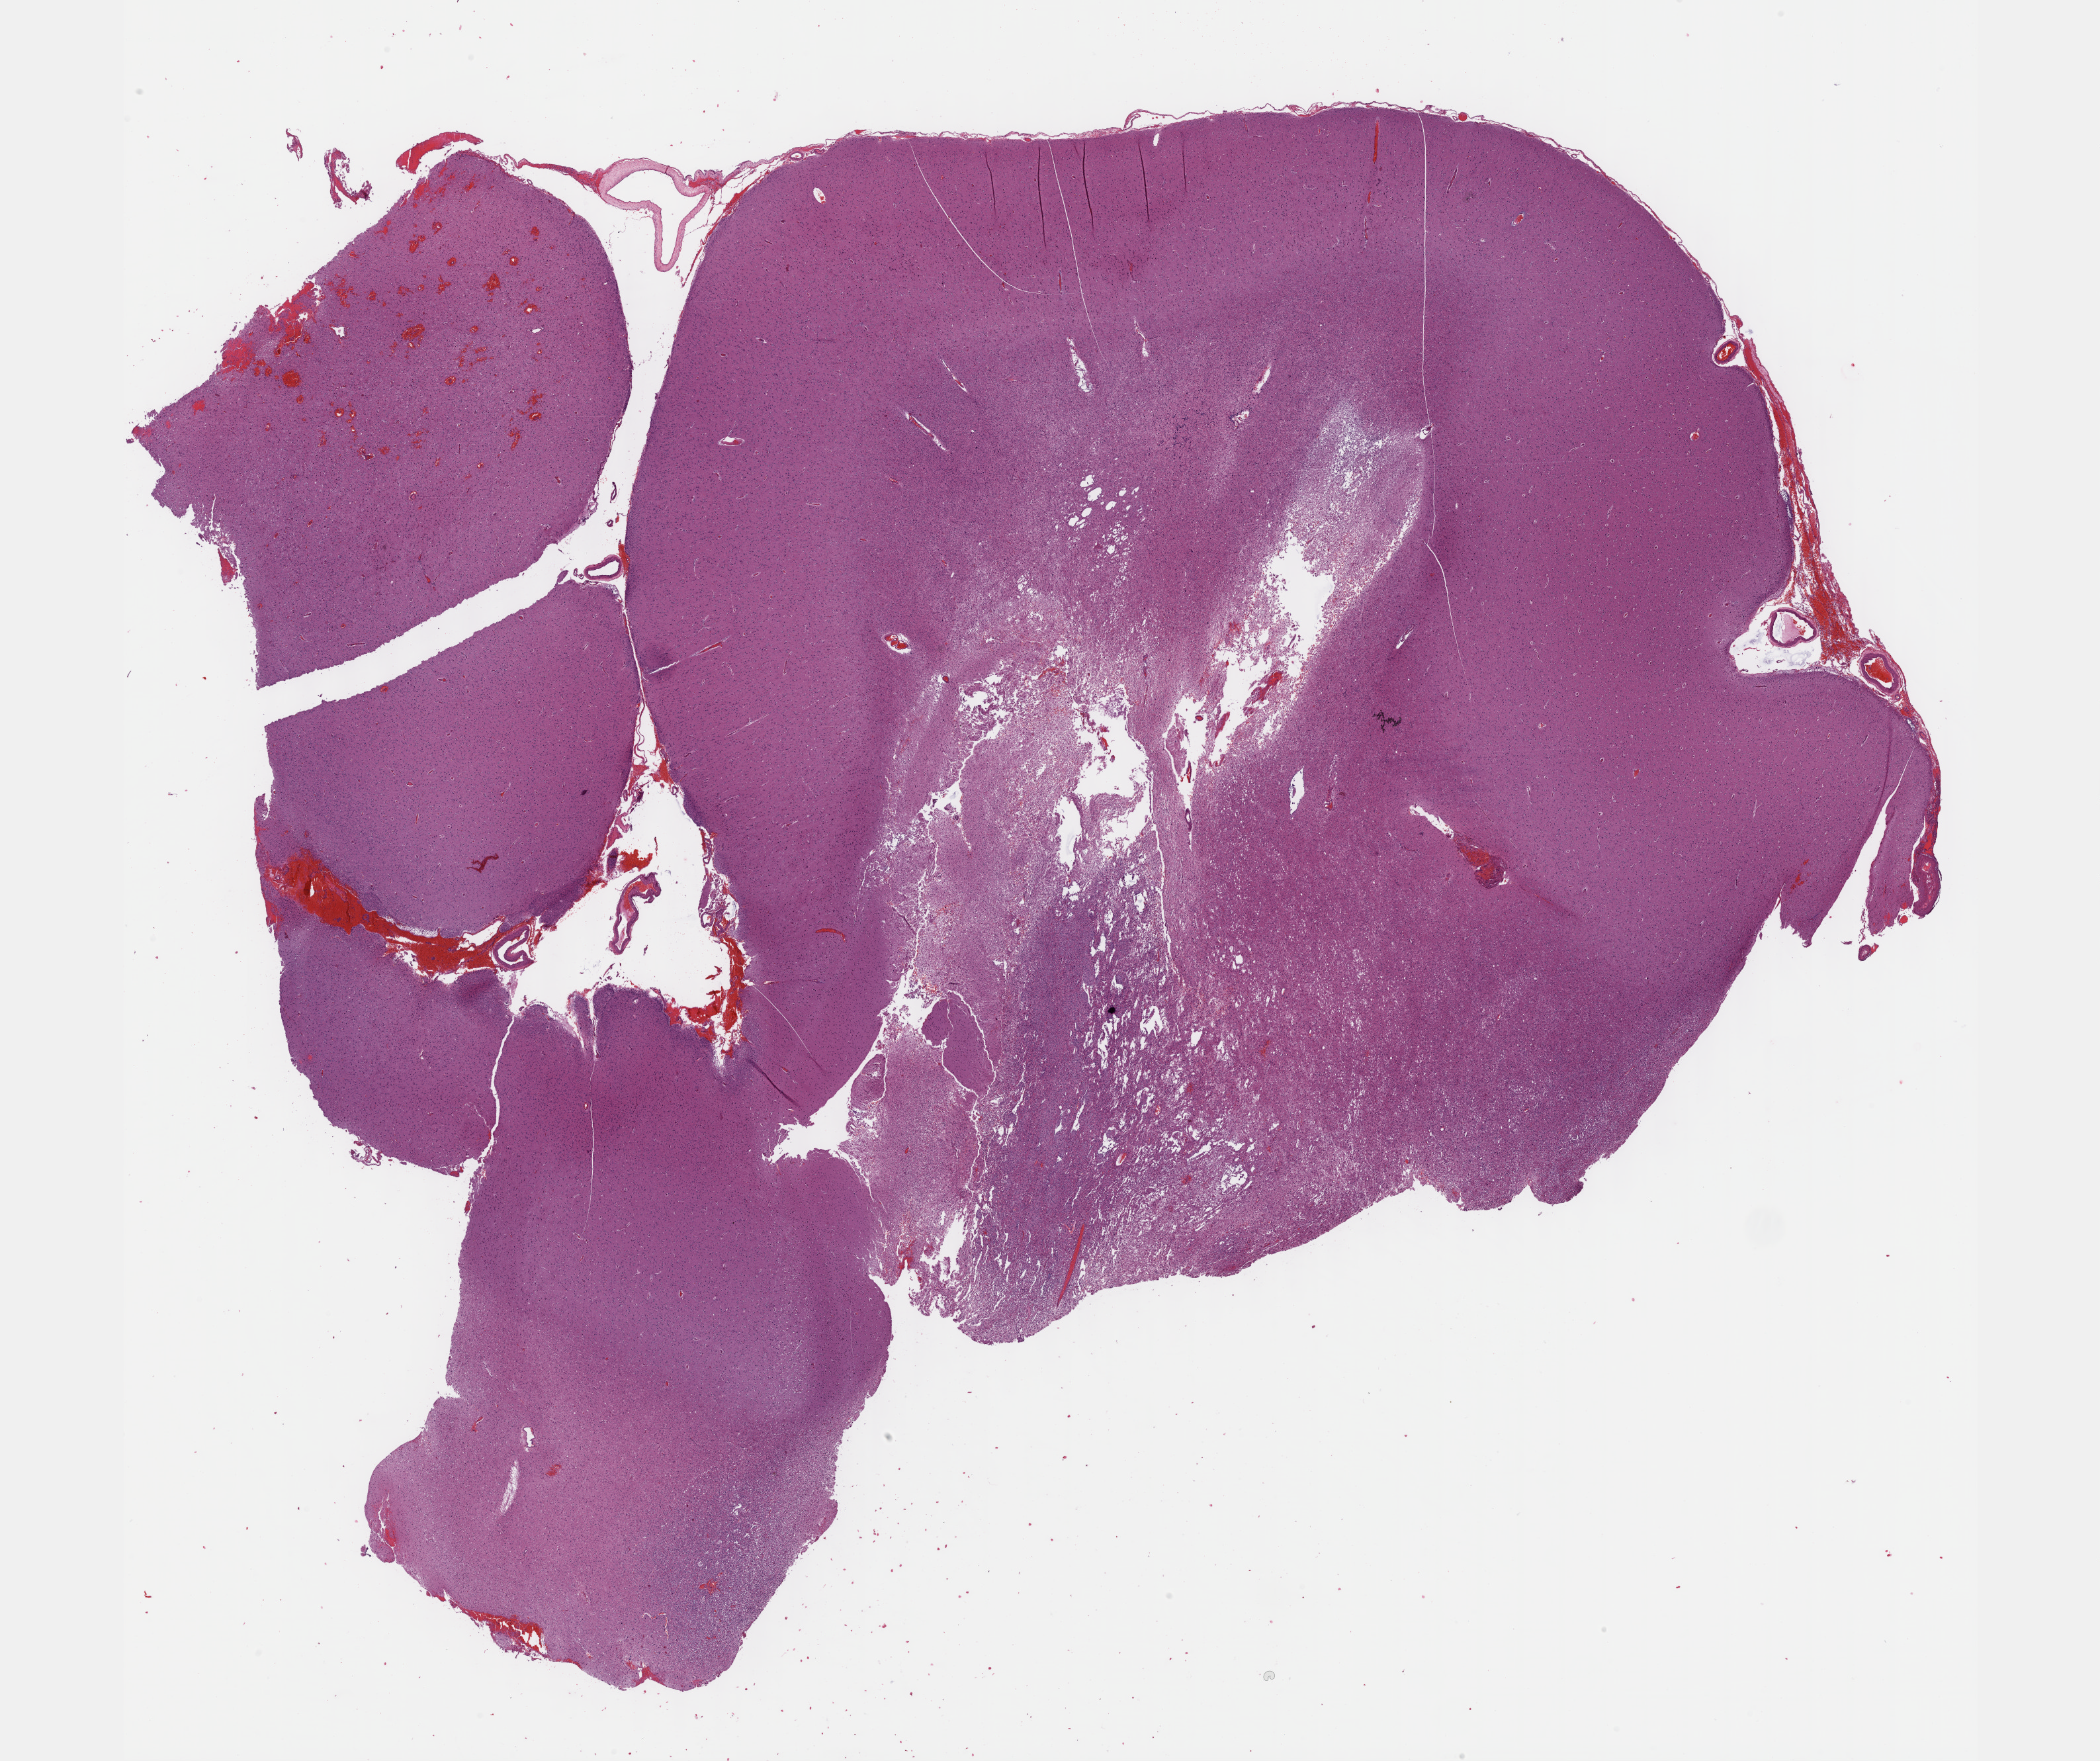
Whole-slide histology image, Hematoxylin and eosin (H&E) stained, low-resolution overview of the scanned area, about 25.7 x 21.5 mm (from a 40x scan); formalin-fixed paraffin-embedded (FFPE) diagnostic section; sample: primary tumour, brain. Male patient; age at initial diagnosis 60 years.
Histologic diagnosis: Oligodendroglioma, anaplastic (cerebrum).